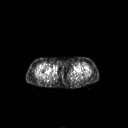
FDG PET of an extremity soft-tissue mass (from a PET/CT study), one axial slice; slice 243 of 311 in the series (ordered by position); 128 × 128 image matrix, field of view 700 × 700 mm. Female patient, age 78 years. Case-level facts recorded for this patient, not image findings: histological type: leiomyosarcoma; grade: intermediate; site of the primary tumour: parascapusular.
Structures marked on this image (expert contour drawn on MRI and transferred to this co-registered scan by the dataset authors):
- gross tumour volume including surrounding oedema: bounding box (x1, y1, x2, y2) in pixels: (52, 65, 59, 71)
- gross tumour volume (mass): (53, 65, 59, 70)